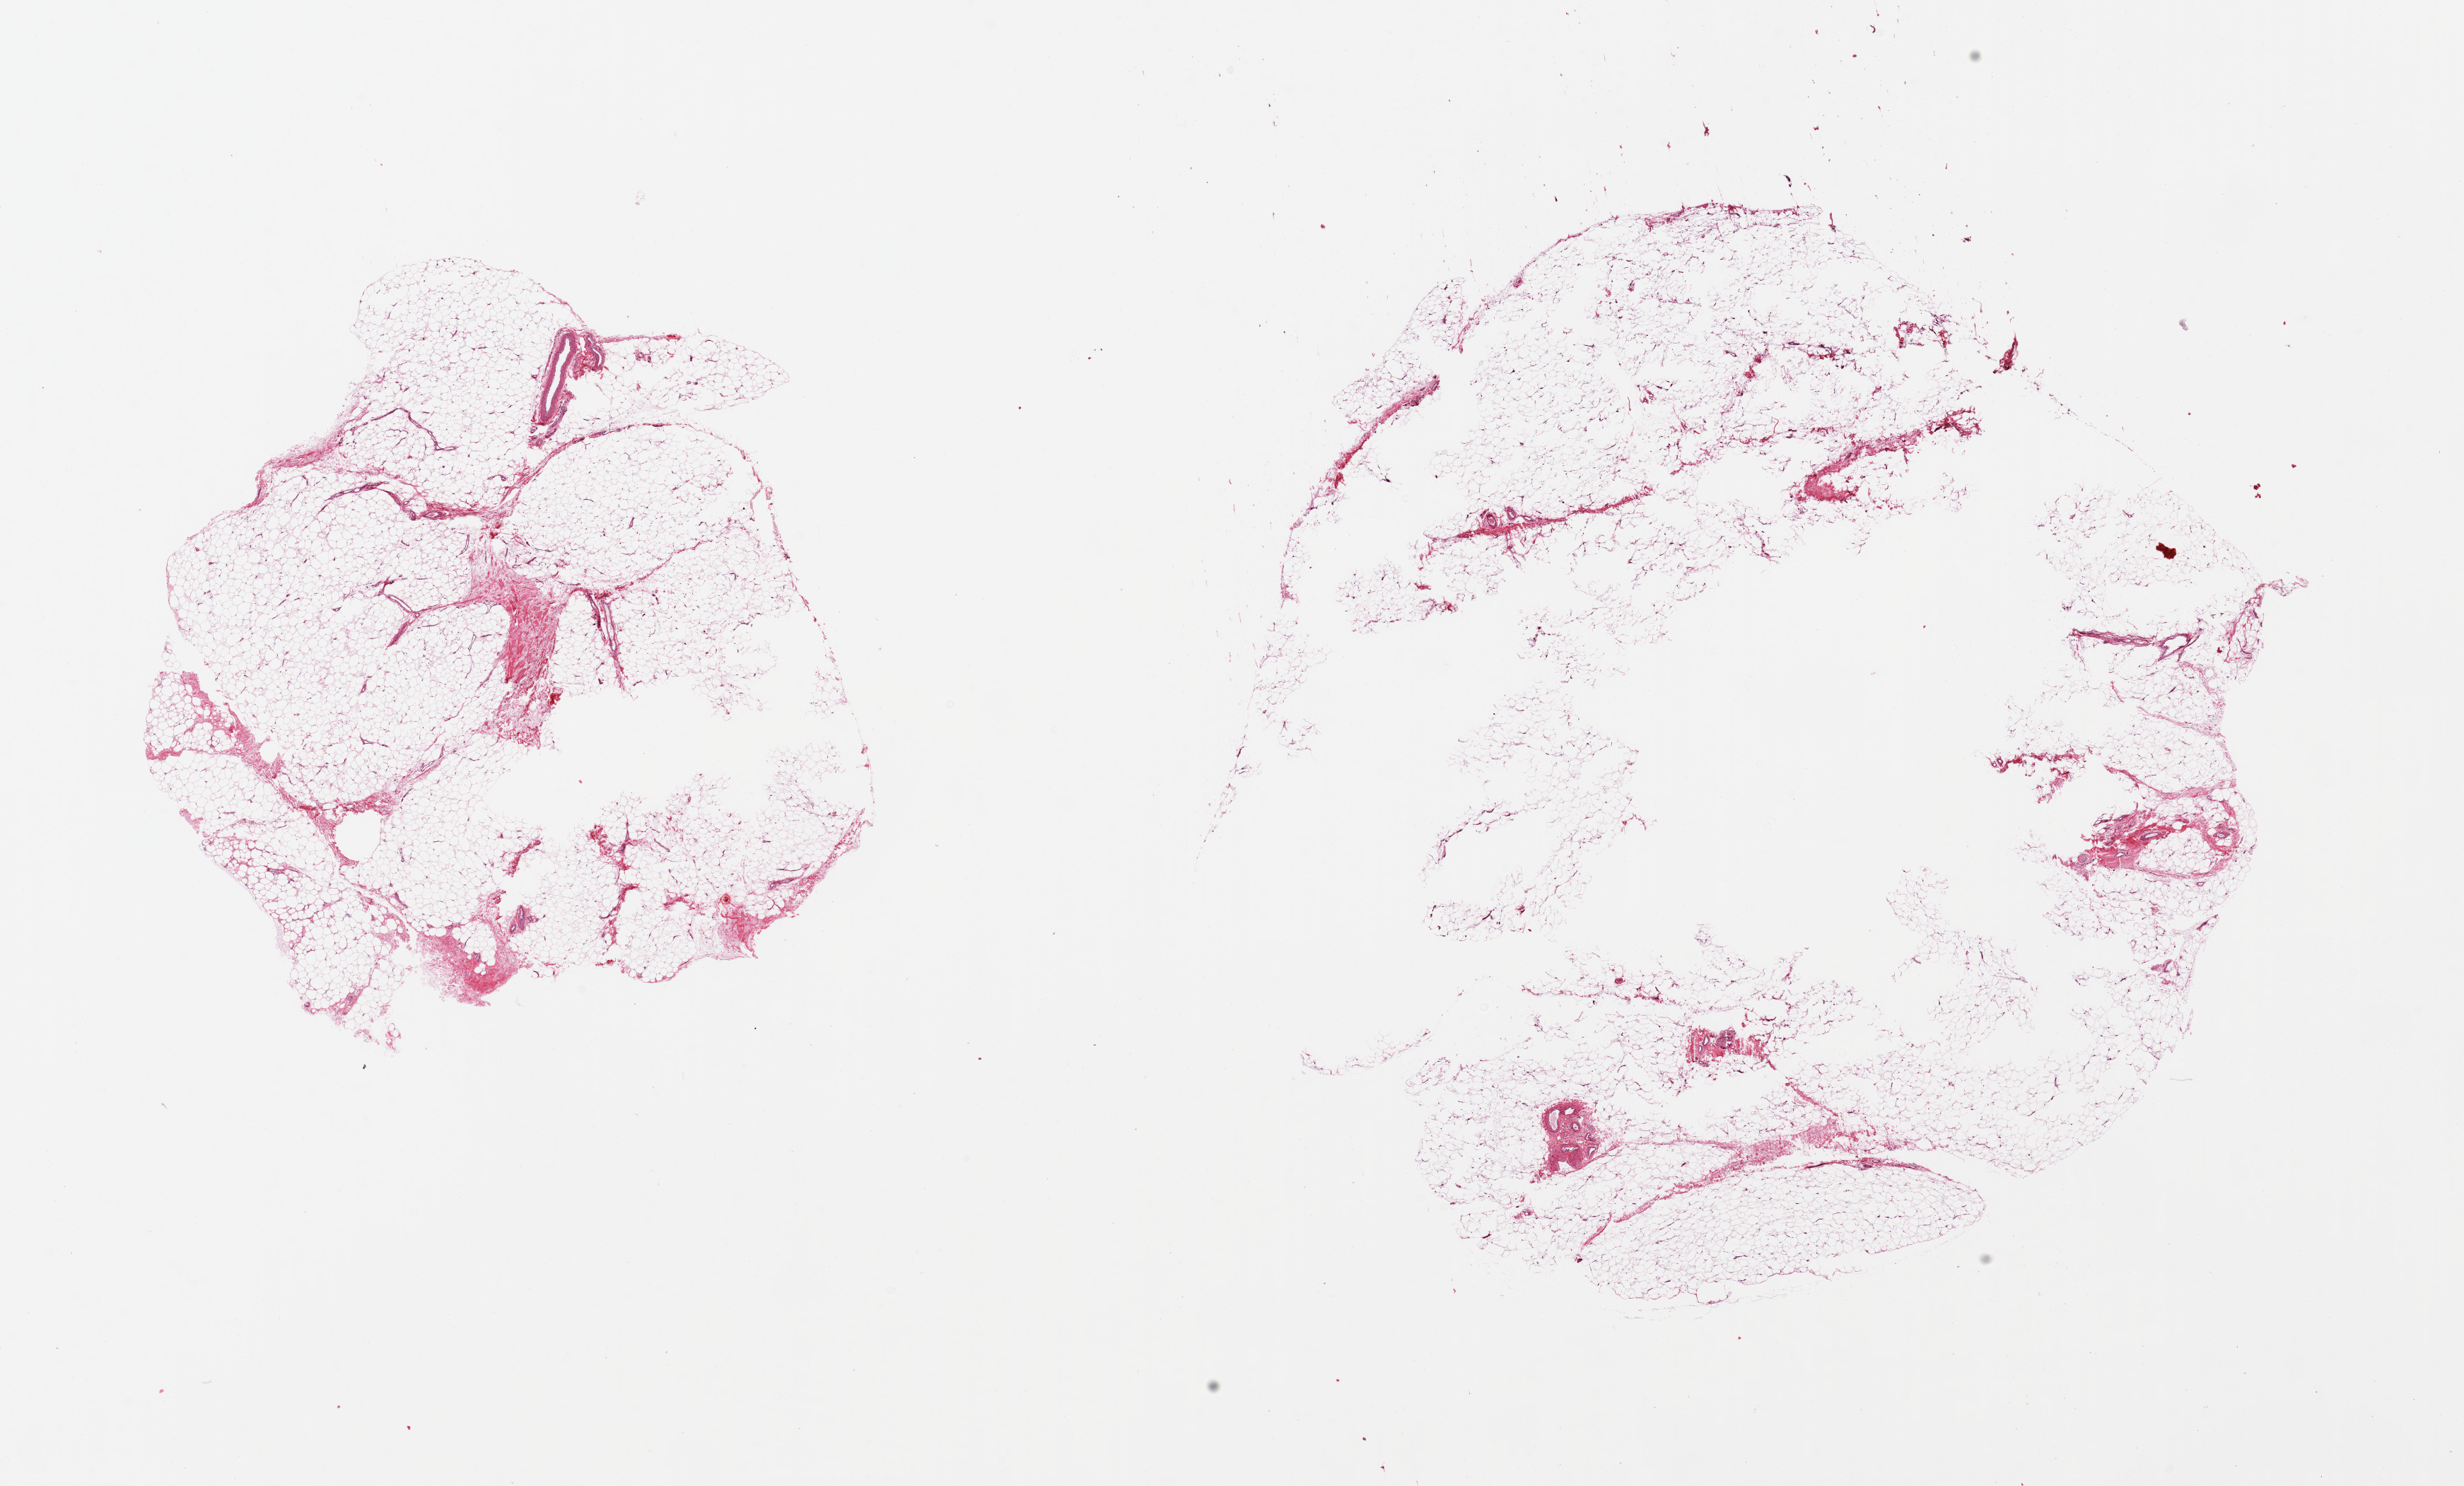
Whole-slide image, H&E stain — shown as a low-resolution overview of the whole scanned area (about 27.6 x 16.6 mm). PAXgene-fixed paraffin-embedded (PFPE) section. Section of adipose tissue (target tissue). Tissue donor sample. Male donor.
Review note (as recorded): 2 pieces; multiple 'empty' defects ; 10% fibrous content.